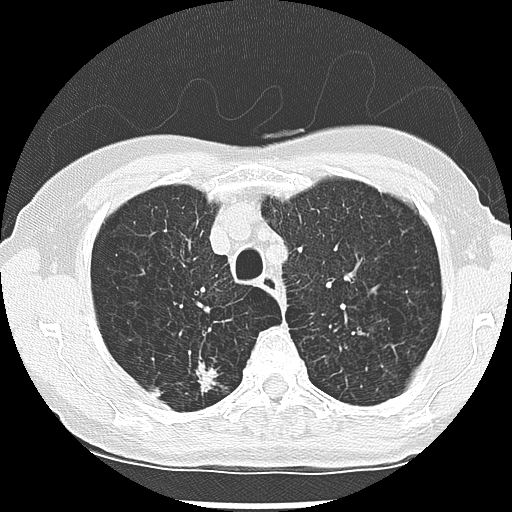
Low-dose screening chest CT, one axial slice. Position 214 of 265 along the scan axis. Reconstruction kernel LUNG. 120 kVp. Lung window (W 1500 / L -600 HU). 2.5 mm slice thickness. 512 × 512 image matrix, field of view 300 × 300 mm.
Structures marked on this image (expert manual segmentation):
- lesion 1 (nodule, upper lobe of right lung): bounding box <196,363,217,393> (left, top, right, bottom; pixels)